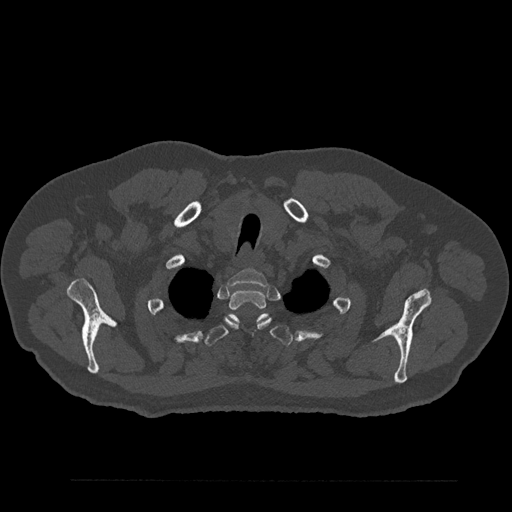
CT including the spine, one axial slice; slice 710 of 797 in the series (ordered by position); 120 kVp; bone window (W 1800 / L 400 HU); 0.5 mm slice thickness; 512 × 512 image matrix, field of view 430 × 430 mm. Male patient, age 61 years. From the clinical record (not read from this slice): primary cancer: prostate.
Outlined on this slice (semi-automatic segmentation, software-assisted and operator-edited):
- T1 vertebra: bounding box [x1, y1, x2, y2] px = [228, 269, 268, 286]
- T2 vertebra: [225, 289, 271, 329]
- T3 vertebra: [205, 313, 292, 345]